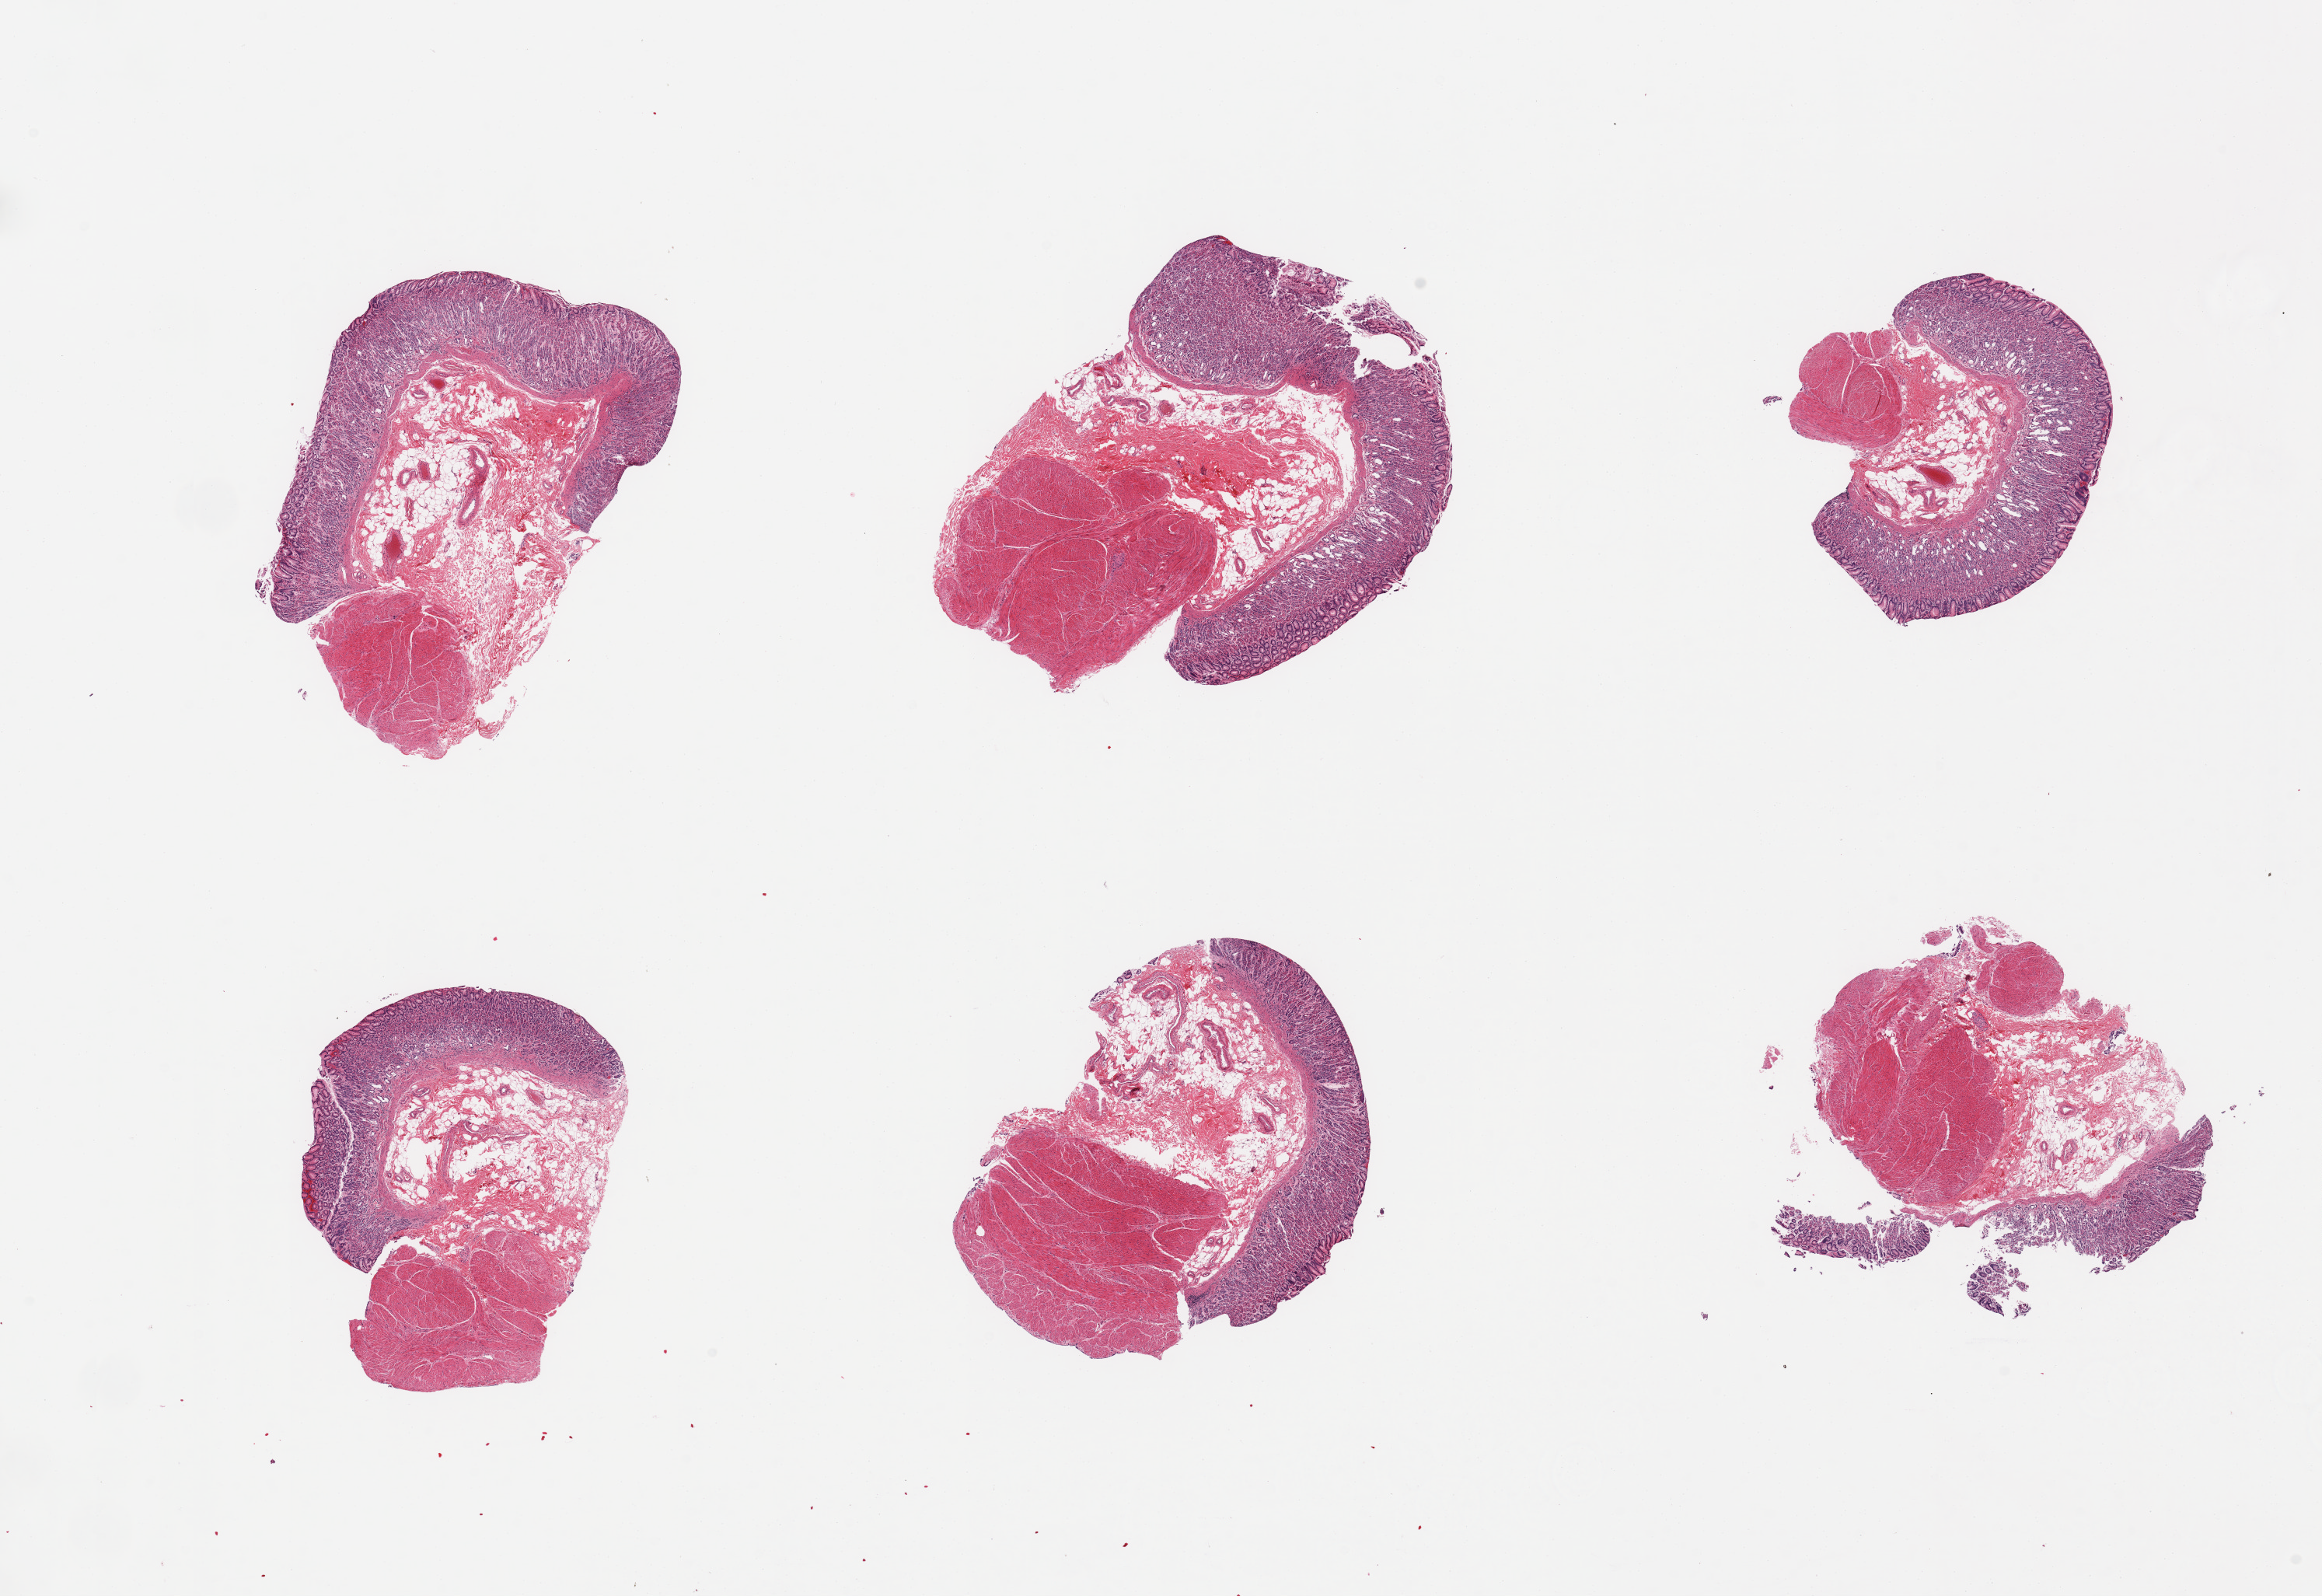
Haematoxylin and eosin whole-slide image, brightfield, whole scanned area (about 23.6 x 16.2 mm, from a 20x scan) shown as a low-resolution overview, PAXgene-fixed, paraffin-embedded tissue, section of stomach (target tissue), donor tissue sample. Donor sex: male.
Reviewer comment on this tissue sample: 6 pieces; mucosa and muscularis.